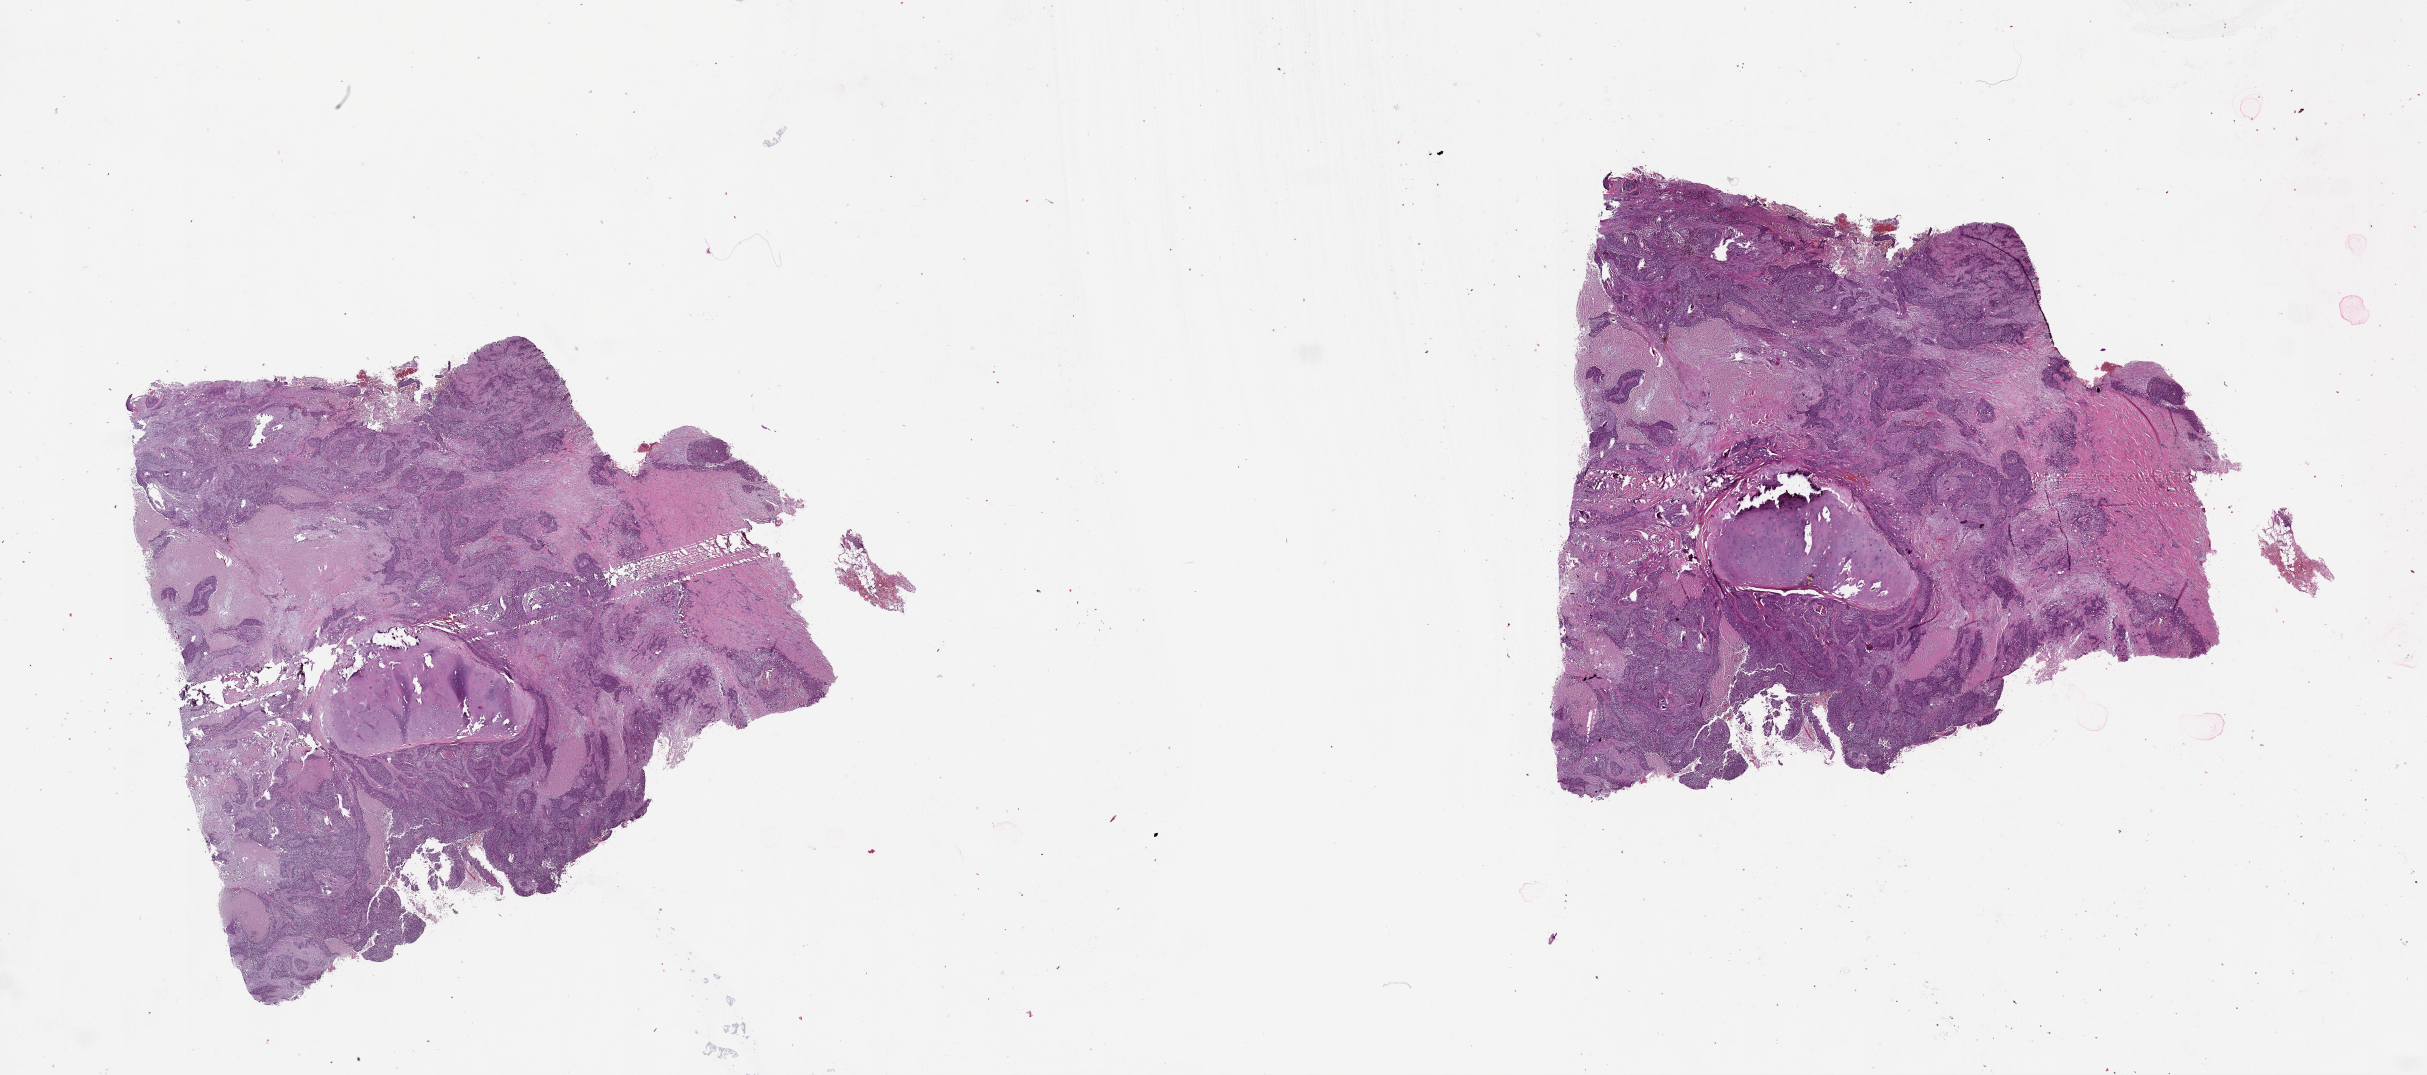
Whole-slide histology image, H&E-stained — low-resolution overview of the scanned area, about 39.1 x 17.3 mm (from a 20x scan). Tumour tissue sample, lung. Patient: male, age 58 years.
Patient diagnosis (cohort enrolment): squamous cell carcinoma (lung).